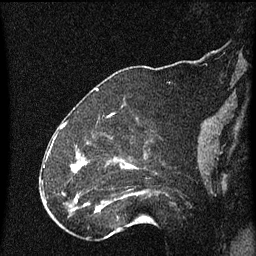
Breast MRI (dynamic contrast-enhanced), one sagittal slice; position 20 of 60 along the scan axis; dynamic contrast-enhanced series, image 2 of 4 at this slice position (ordered by acquisition); 1.5 T; TE 4.2 ms, TR 8 ms; 2 mm slice thickness; 256 × 256 image matrix, field of view 180 × 180 mm. Patient: female, 52 years.
Outlined on this slice (semi-automatic segmentation, software-assisted and operator-edited):
- analysis volume of interest (the breast-tissue region the enhancement analysis was run in; not a lesion): bounding box (x1, y1, x2, y2) in pixels: (73, 148, 153, 219)
- tumour enhancement mask (voxels above the 70 % enhancement threshold inside the analysis volume of interest): (73, 162, 136, 211)